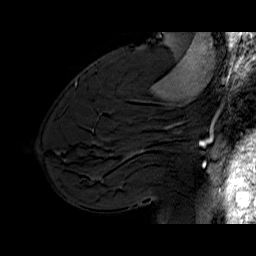
Breast MRI (dynamic contrast-enhanced), one sagittal slice; dynamic contrast-enhanced series, time point 2 of 6 at this slice position (early post-contrast); 1.5 T; TE 6.5 ms, TR 33 ms; 256 × 256 image matrix, field of view 200 × 200 mm. Female patient. Case-level facts recorded for this patient, not image findings: setting: breast cancer imaged before/during neoadjuvant chemotherapy; receptor status: HER2-positive.
Annotated regions visible in this slice (semi-automatic segmentation, software-assisted and operator-edited):
- analysis volume of interest (the breast-tissue region the enhancement analysis was run in; not a lesion): box from (x=113, y=112) to (x=174, y=170) px
- tumour enhancement mask (voxels above the 100 % enhancement threshold inside the analysis volume of interest): (x=164, y=124)–(x=174, y=129)